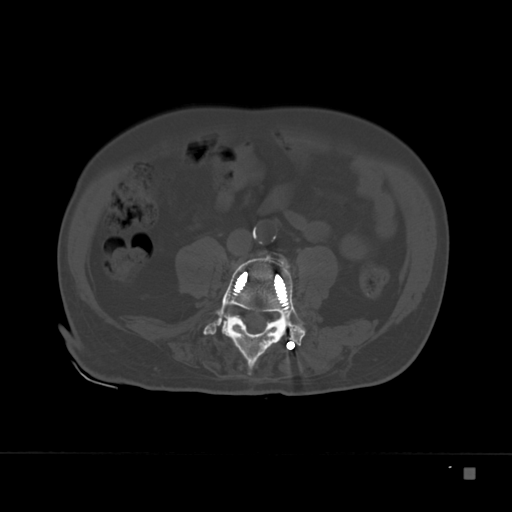
CT including the spine, one axial slice. Slice 44 of 332 in the series (ordered by position). 120 kVp. Bone window (W 1800 / L 400 HU). 1.5 mm slice thickness. 512 × 512 image matrix. Male patient, age 72 years. Case-level facts recorded for this patient, not image findings: primary cancer: skeletal.
Annotated regions visible in this slice (semi-automatic segmentation, software-assisted and operator-edited):
- L4 vertebra: bounding box (x1, y1, x2, y2) in pixels: (203, 251, 306, 369)